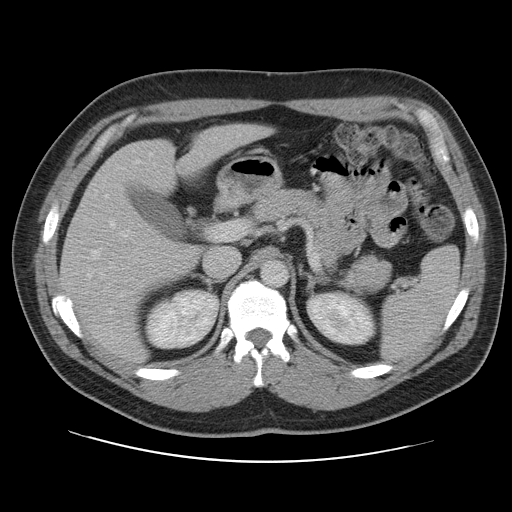
Contrast-enhanced abdominal CT, one axial slice. Slice 67 of 109 in the series (ordered by position). 120 kVp. Intravenous contrast given. Soft-tissue window (W 400 / L 40 HU). 5 mm slice thickness. 512 × 512 image matrix. Male patient, age 35 years. Case-level facts recorded for this patient, not image findings: diagnosis: colorectal cancer liver metastases, imaged before liver resection; multiple liver metastases: yes; largest metastasis: 2.8 cm; chemotherapy before resection: yes.
Structures marked on this image (outlined manually by an expert reader):
- hepatic veins: bounding box <89,161,139,314> (left, top, right, bottom; pixels)
- liver: <61,125,268,361>
- planned liver remnant (the part of the liver to remain after resection): <61,125,268,361>
- portal vein (with intrahepatic branches): <86,229,154,285>